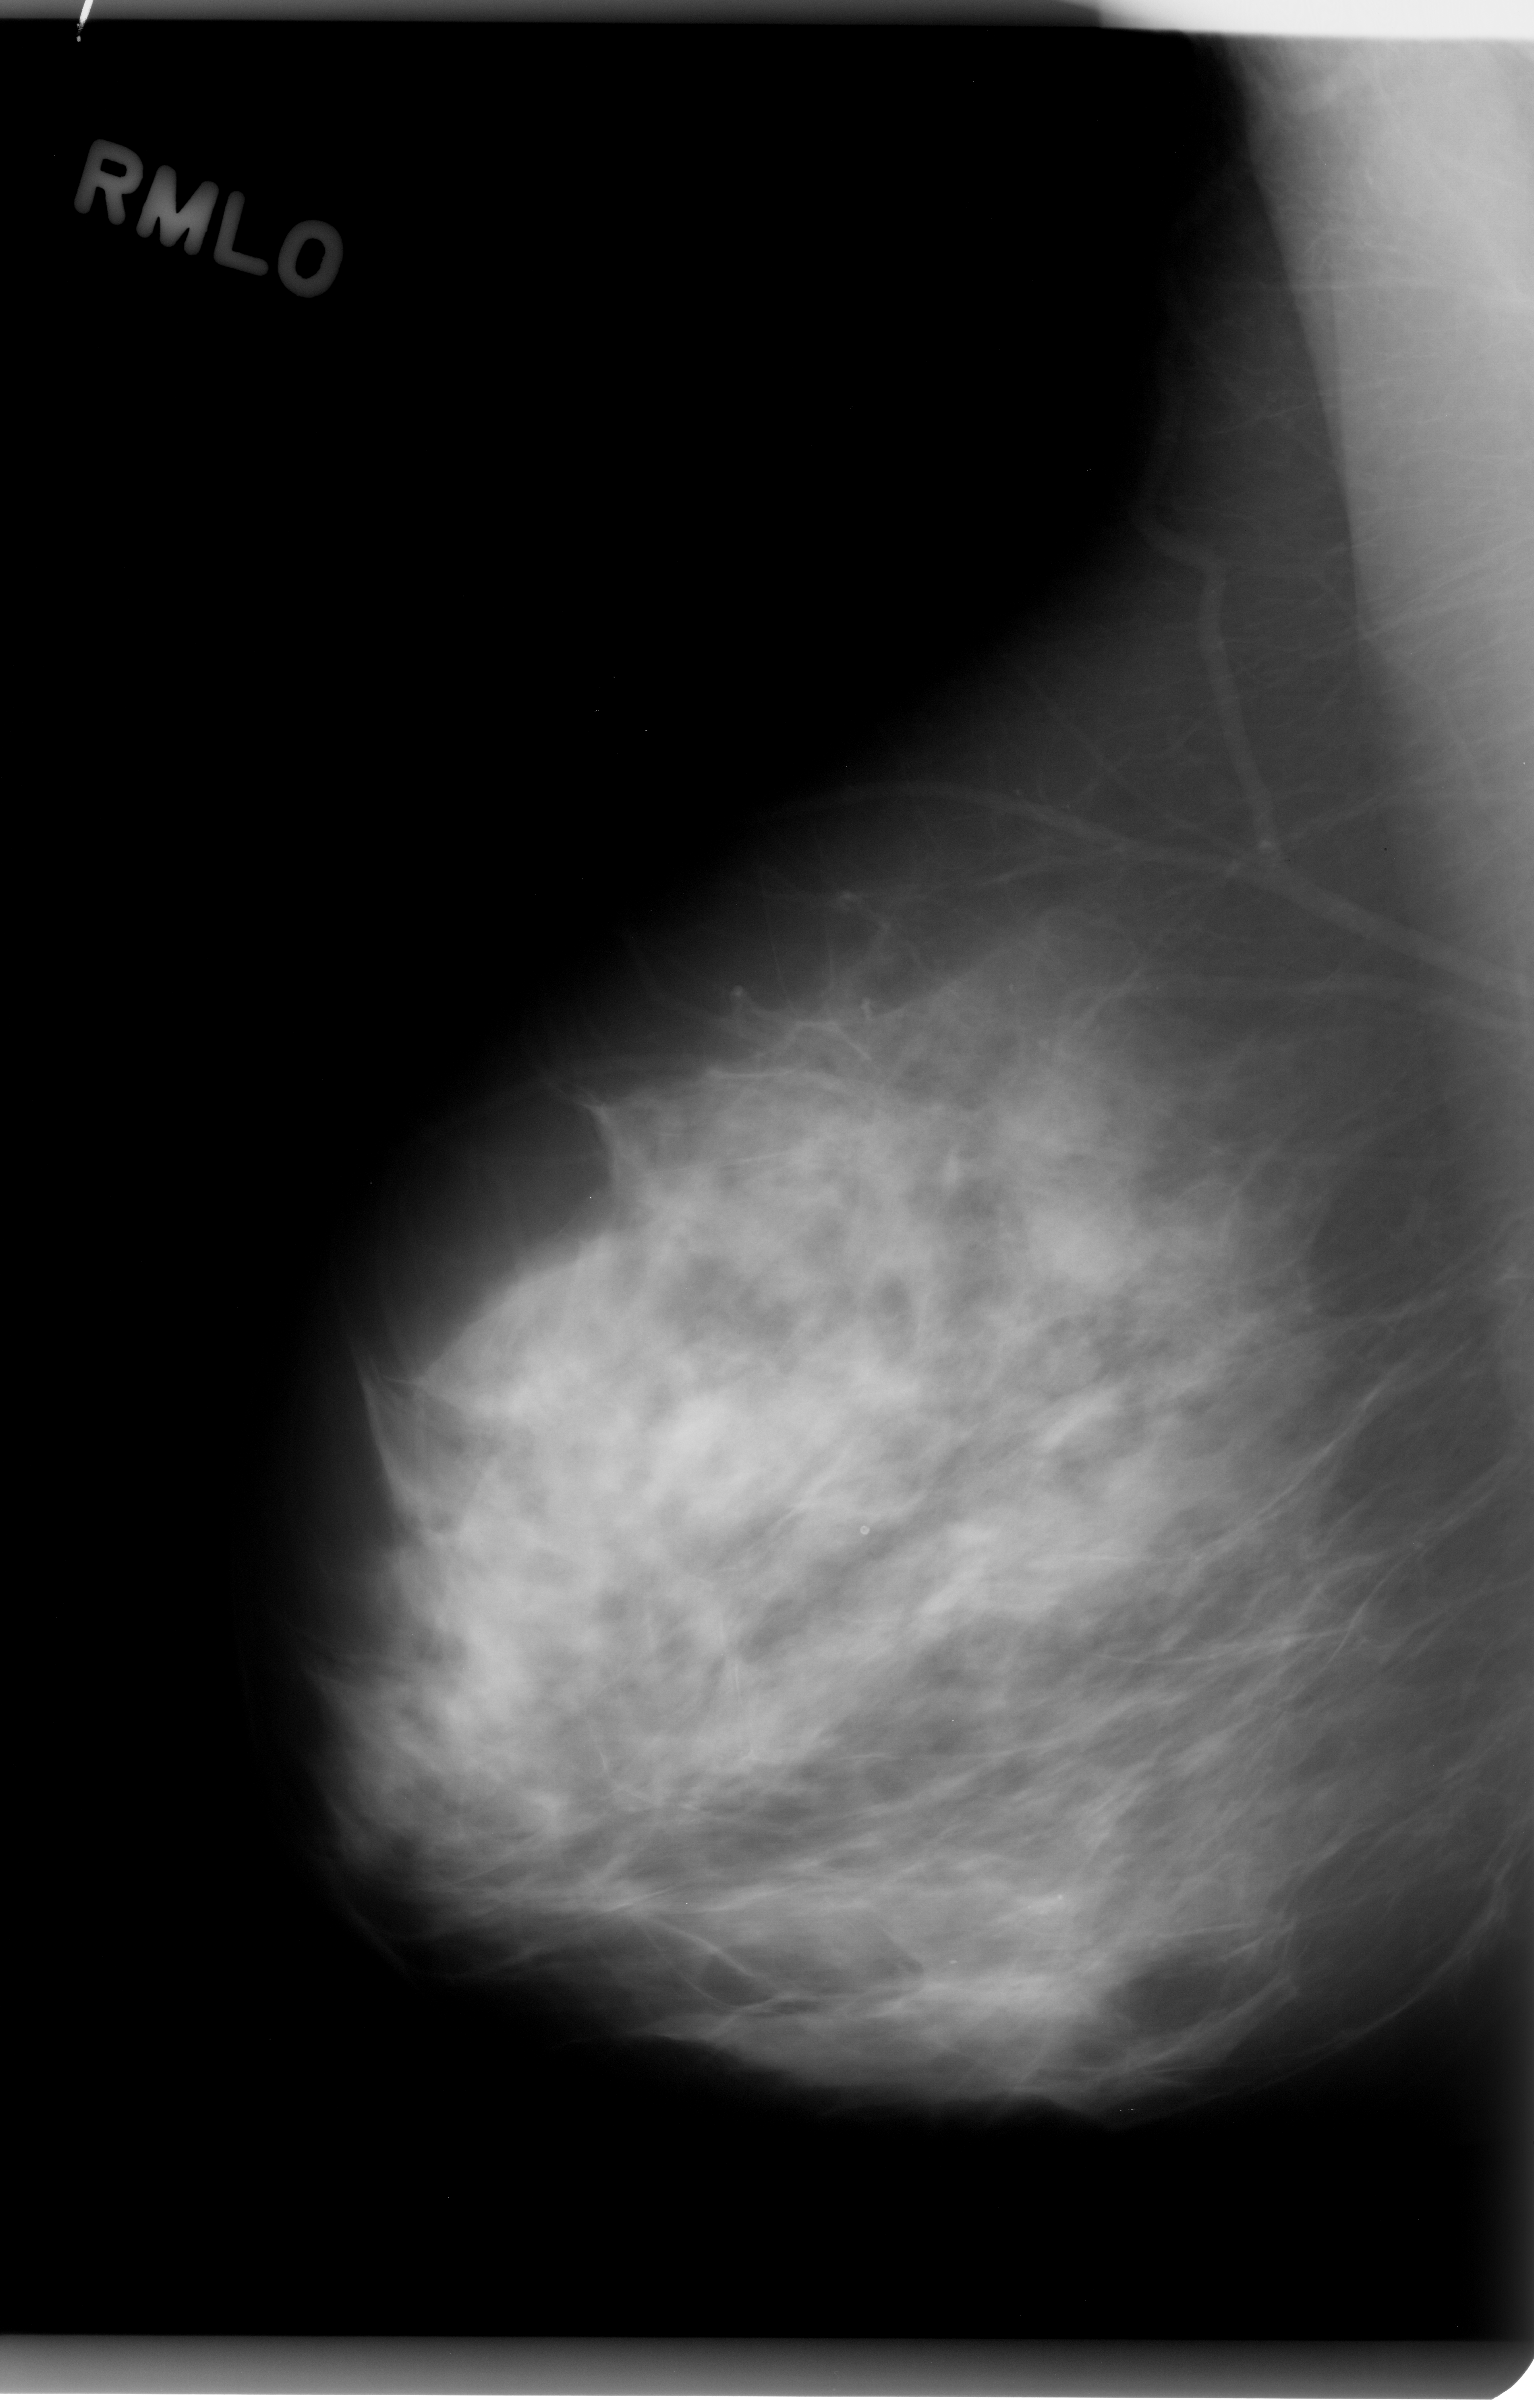
Digitized screen-film mammogram, right breast, mediolateral oblique (MLO) view, BI-RADS breast density category 3 (scale 1–4).
Finding: mass, shape oval, margins microlobulated; BI-RADS assessment category 4; subtlety rating 2 on a 1 (subtle) to 5 (obvious) scale; pathology result (as recorded, not read from the image): benign.